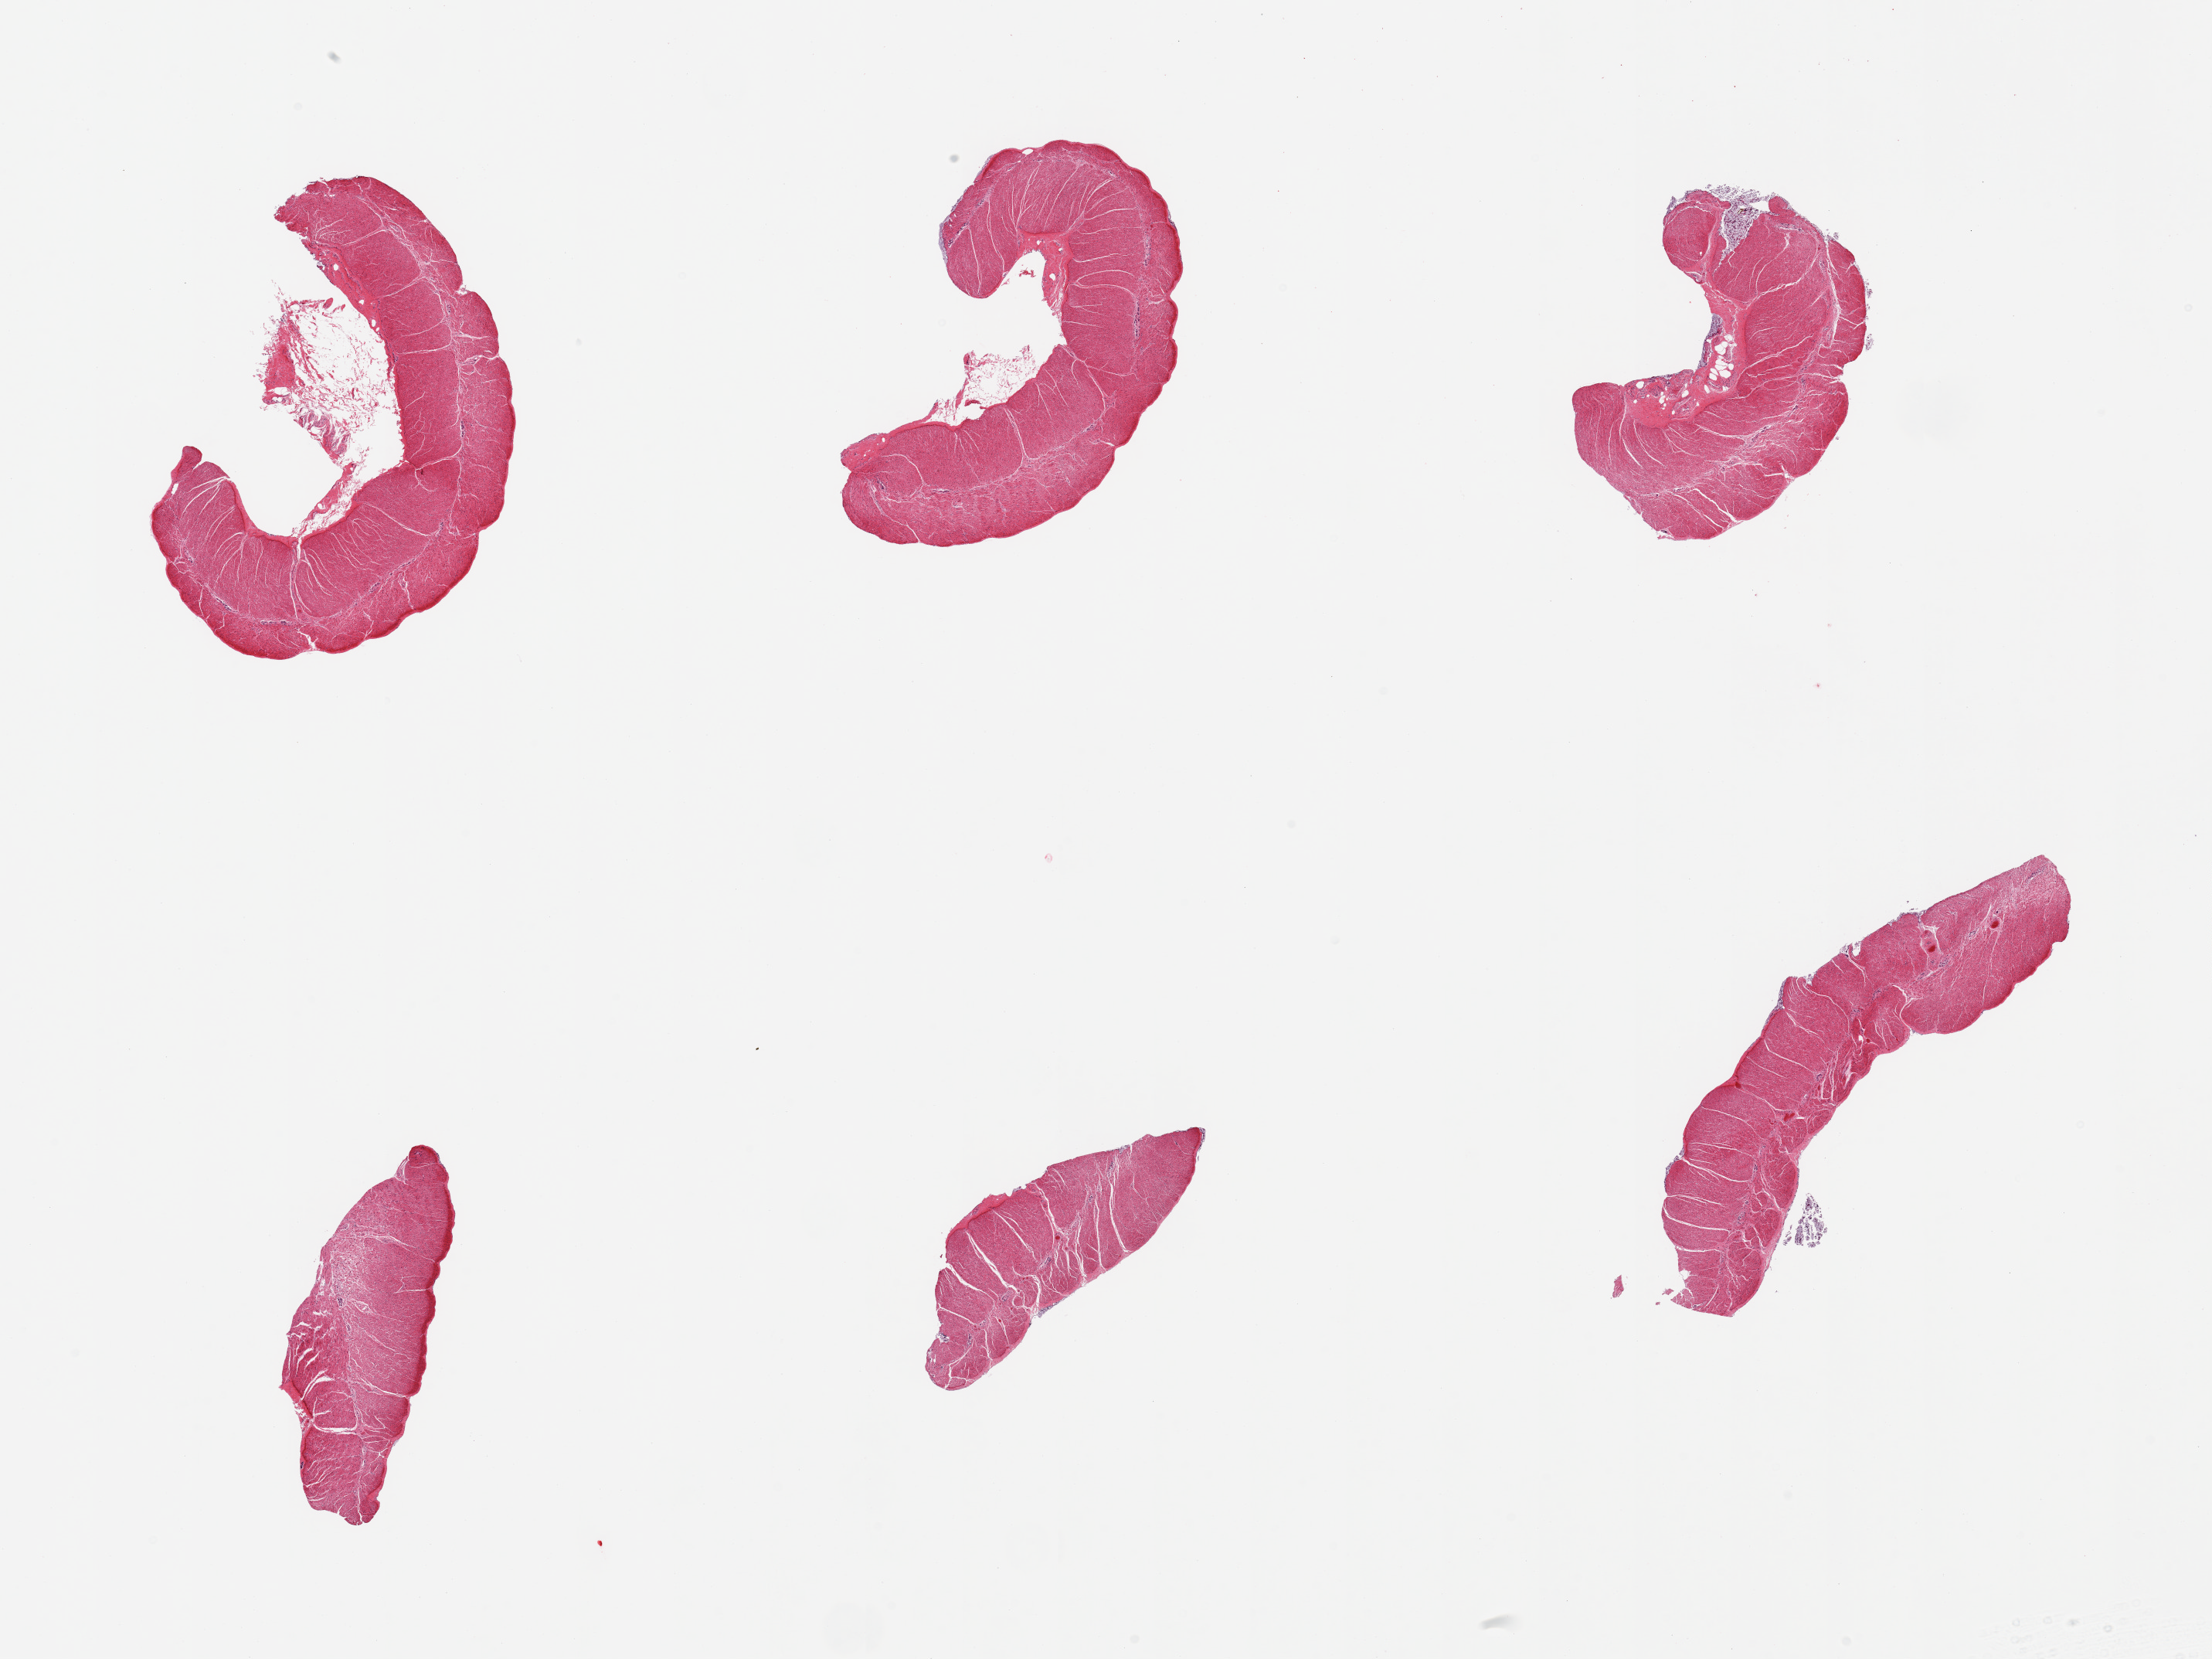
Whole-slide image, hematoxylin and eosin (H&E) stain, shown as a low-resolution overview of the whole scanned area (about 22.6 x 17.0 mm); PAXgene-fixed, paraffin-embedded tissue; section of sigmoid colon (target tissue); tissue donor sample.
Pathologist's review note for this sample: 6 pieces; essentially well trimmed; detached glandular epithelium.